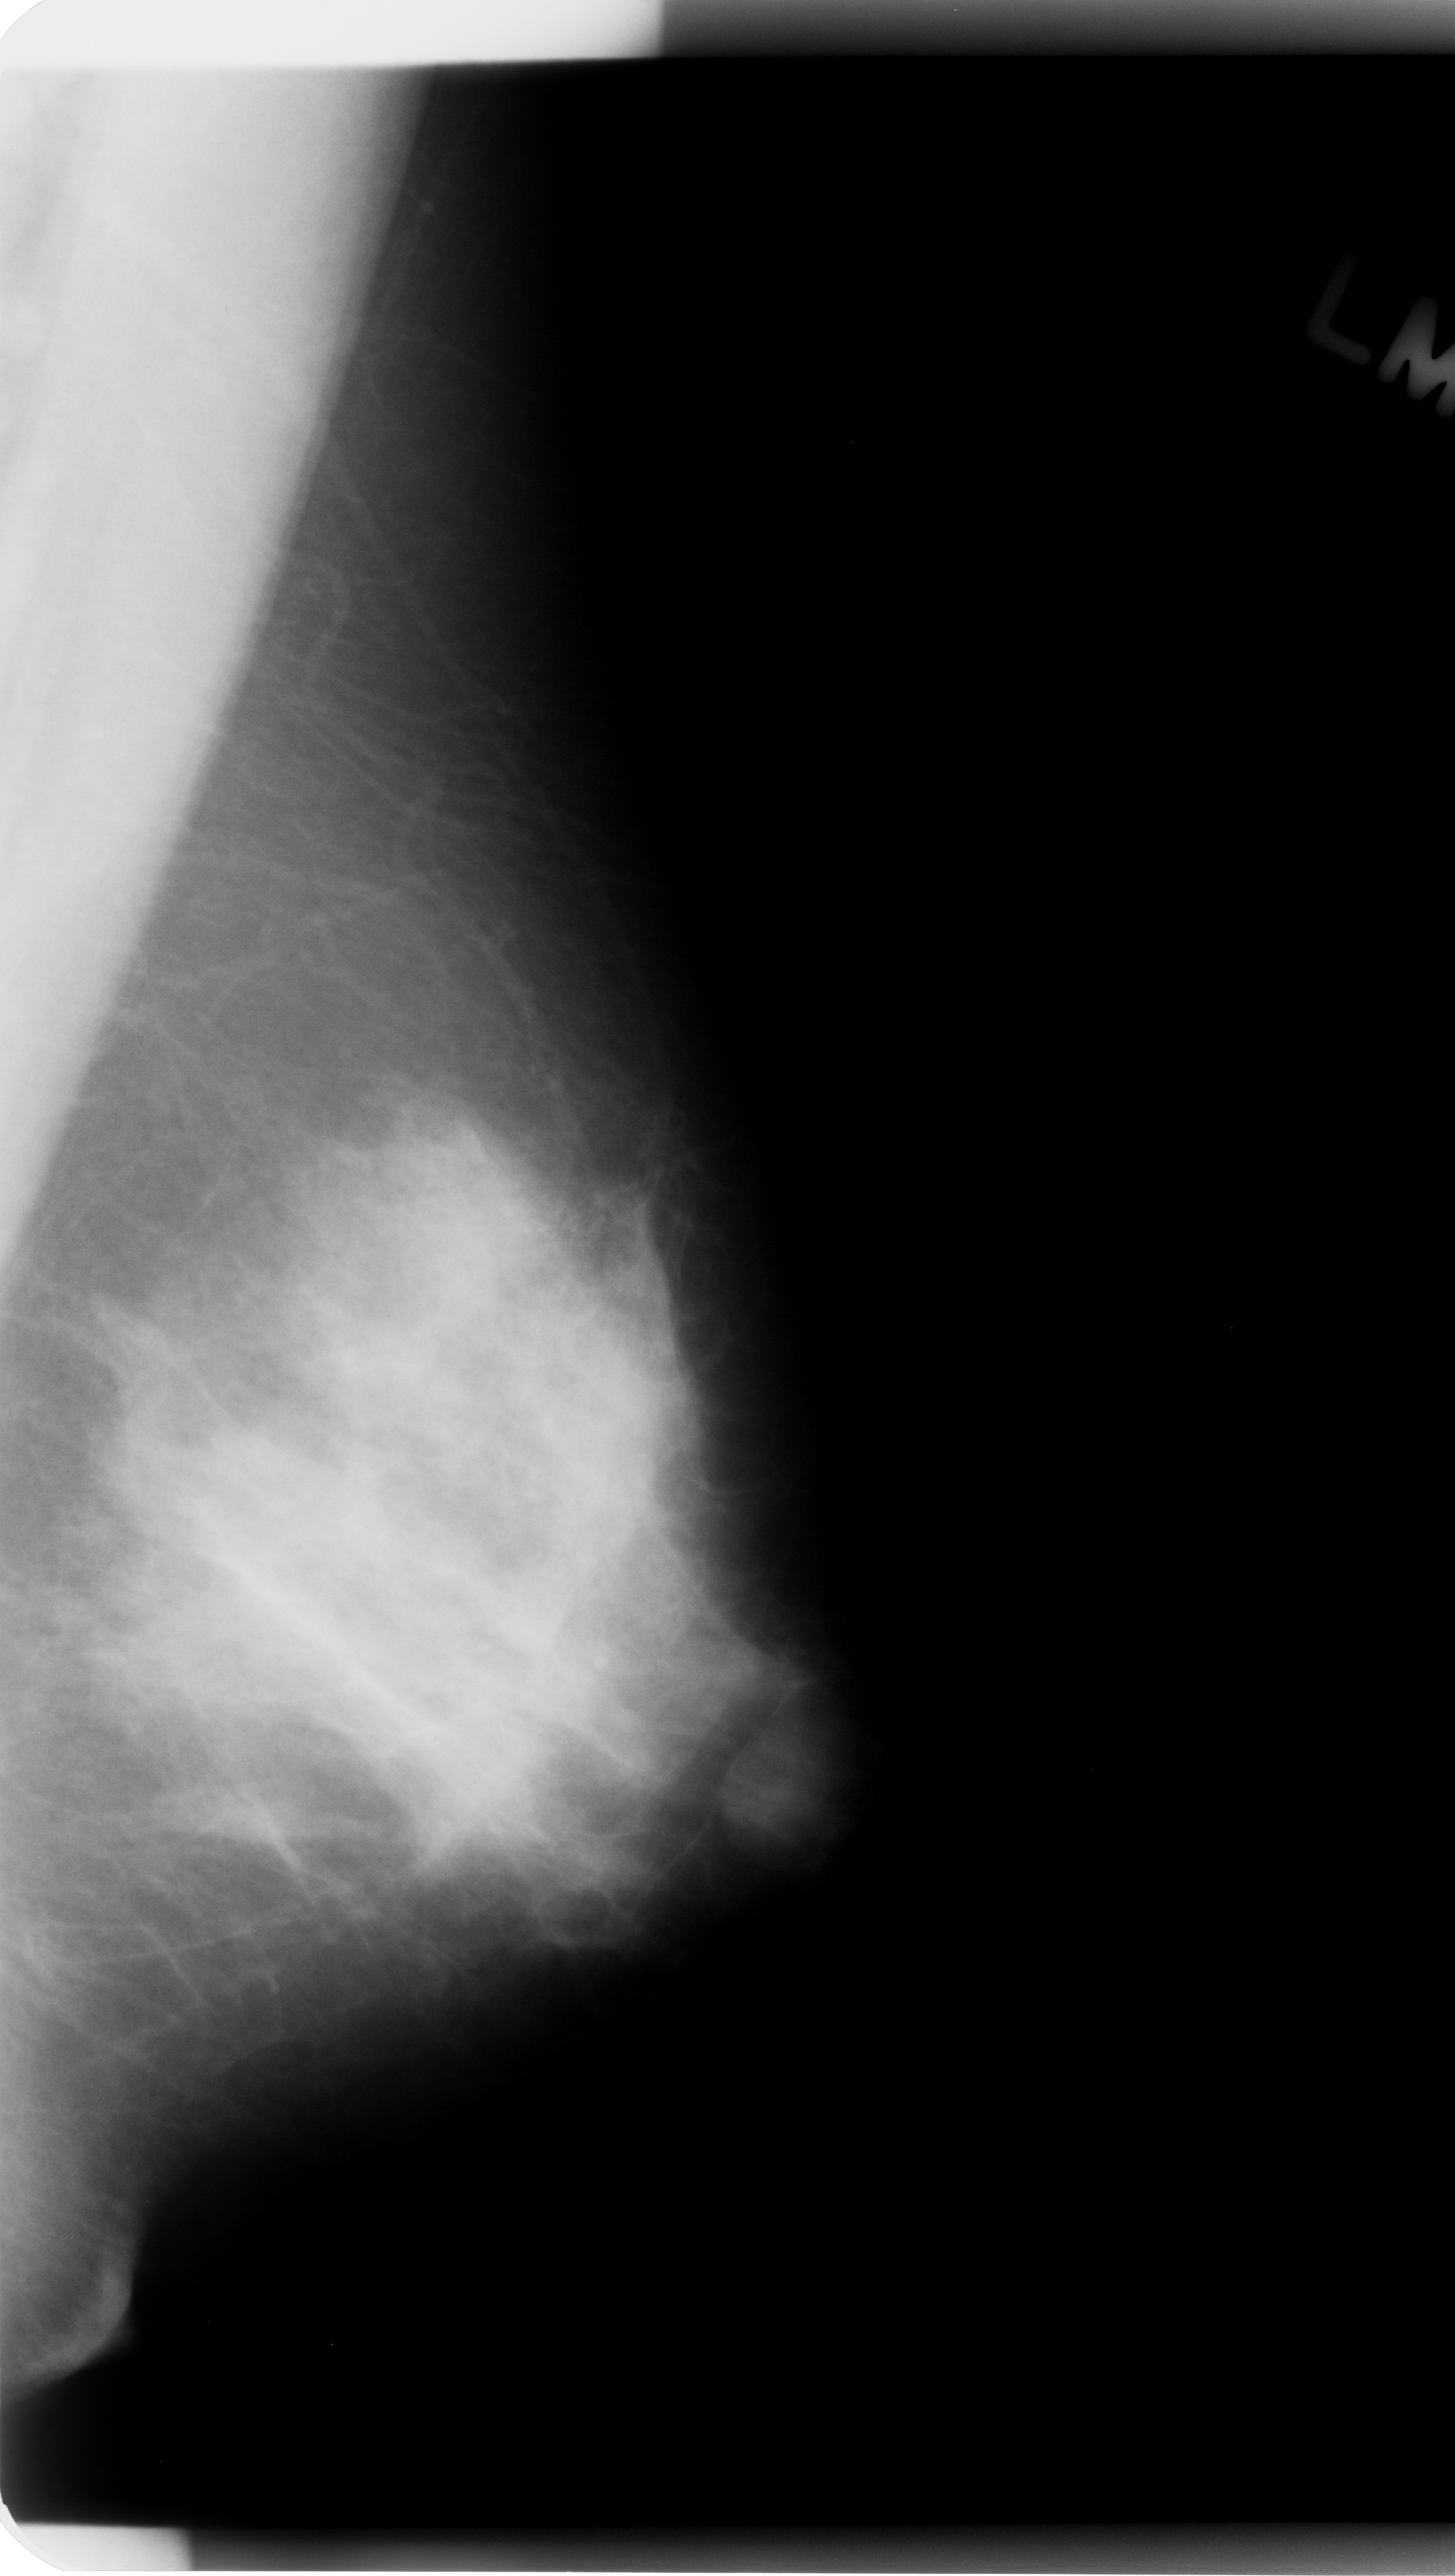
Scanned film-screen mammogram; left breast; MLO view; BI-RADS breast density category 3 (scale 1–4); 1455 × 2576 image matrix.
Marked abnormalities (boxes around the expert regions of interest):
- mass, shape oval, margins circumscribed; BI-RADS assessment category 4; pathology (as recorded): benign: bounding box (x1, y1, x2, y2) in pixels: (713, 1727, 843, 1865)